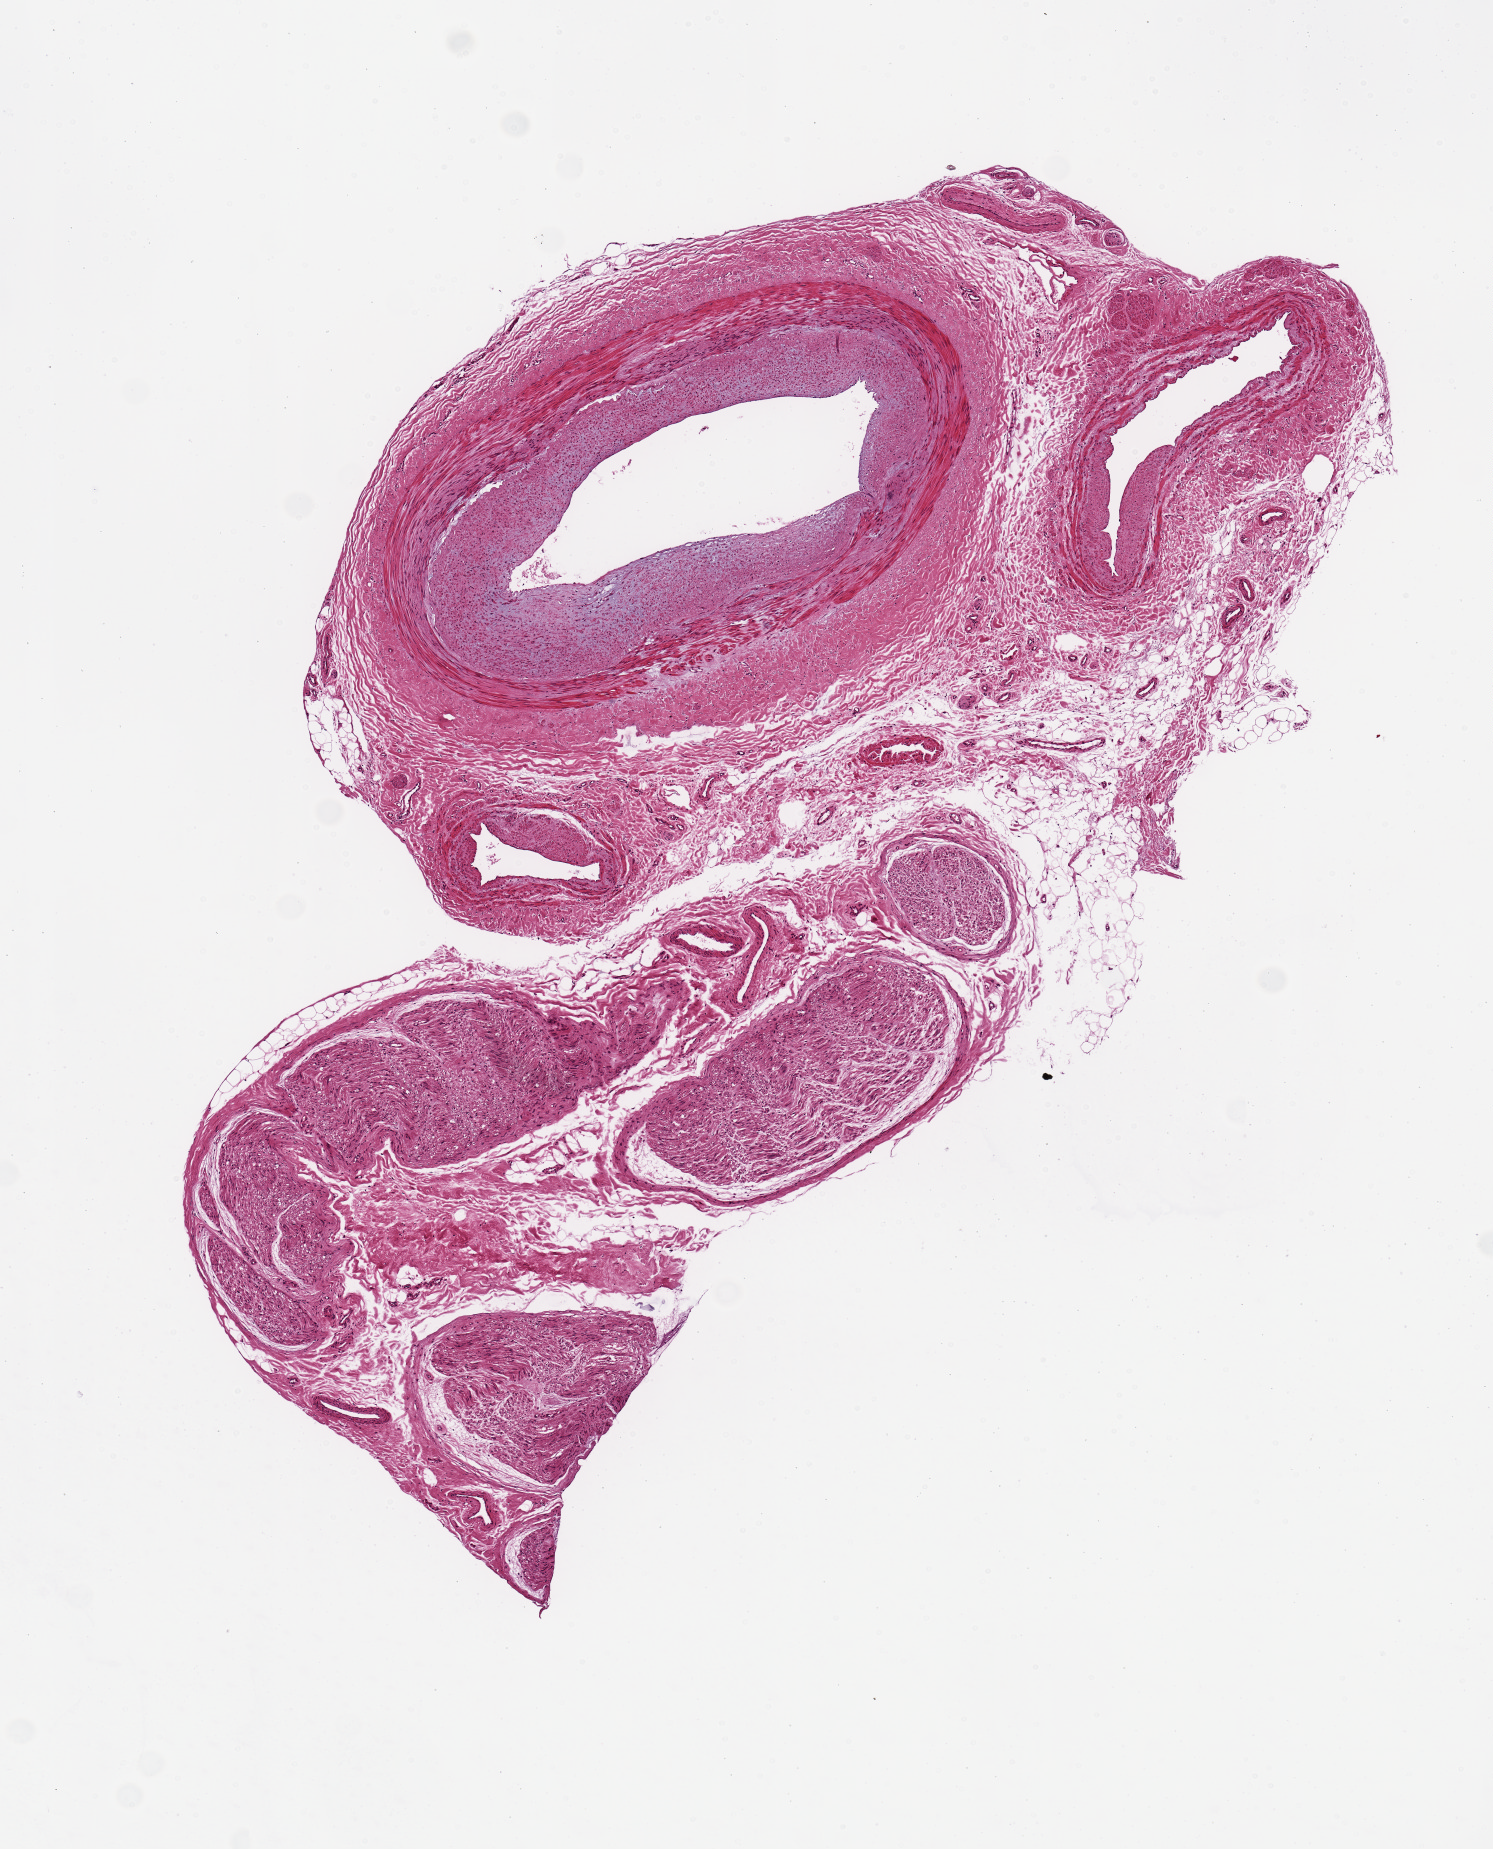
H&E whole-slide image — whole scanned area (about 5.9 x 7.3 mm, slide scanned at 20x) shown as a low-resolution overview; PAXgene-fixed paraffin-embedded (PFPE) section; target tissue: tibial artery; tissue donor sample.
Pathologist's review note for this sample: 0; artery is 24% of area; mostly nerves.